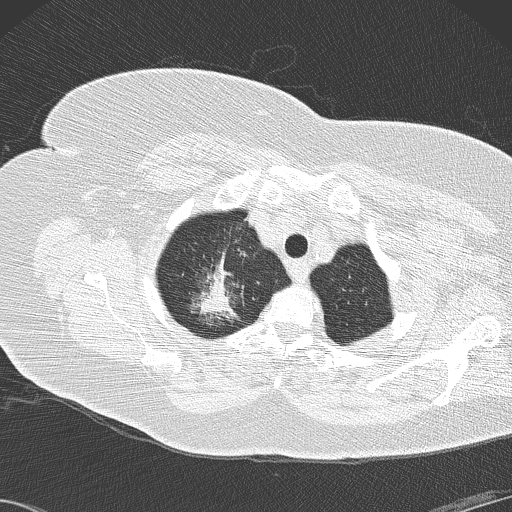
Low-dose screening chest CT, axial slice. Second annual screen. Lung window (W 1500 / L -600 HU). Lung (sharp) reconstruction kernel (B50f). Slice 20 of 146 in the series. Female participant, aged 72 years at enrolment. Former smoker at enrolment.
Expert-annotated lung lesion, bounding box <182,245,259,327> (left, top, right, bottom; pixels). The screening reader recorded 4 non-calcified nodules or masses ≥4 mm on this exam (right lower lobe, right lower lobe, right lower lobe, right upper lobe); which of them this box marks is not recorded. Official screen result: positive, other. Lung cancer was diagnosed 52 days after this screen: bronchiolo-alveolar adenocarcinoma, NOS, right upper lobe, stage IIIB (AJCC 6th edition), 45 mm at pathology.